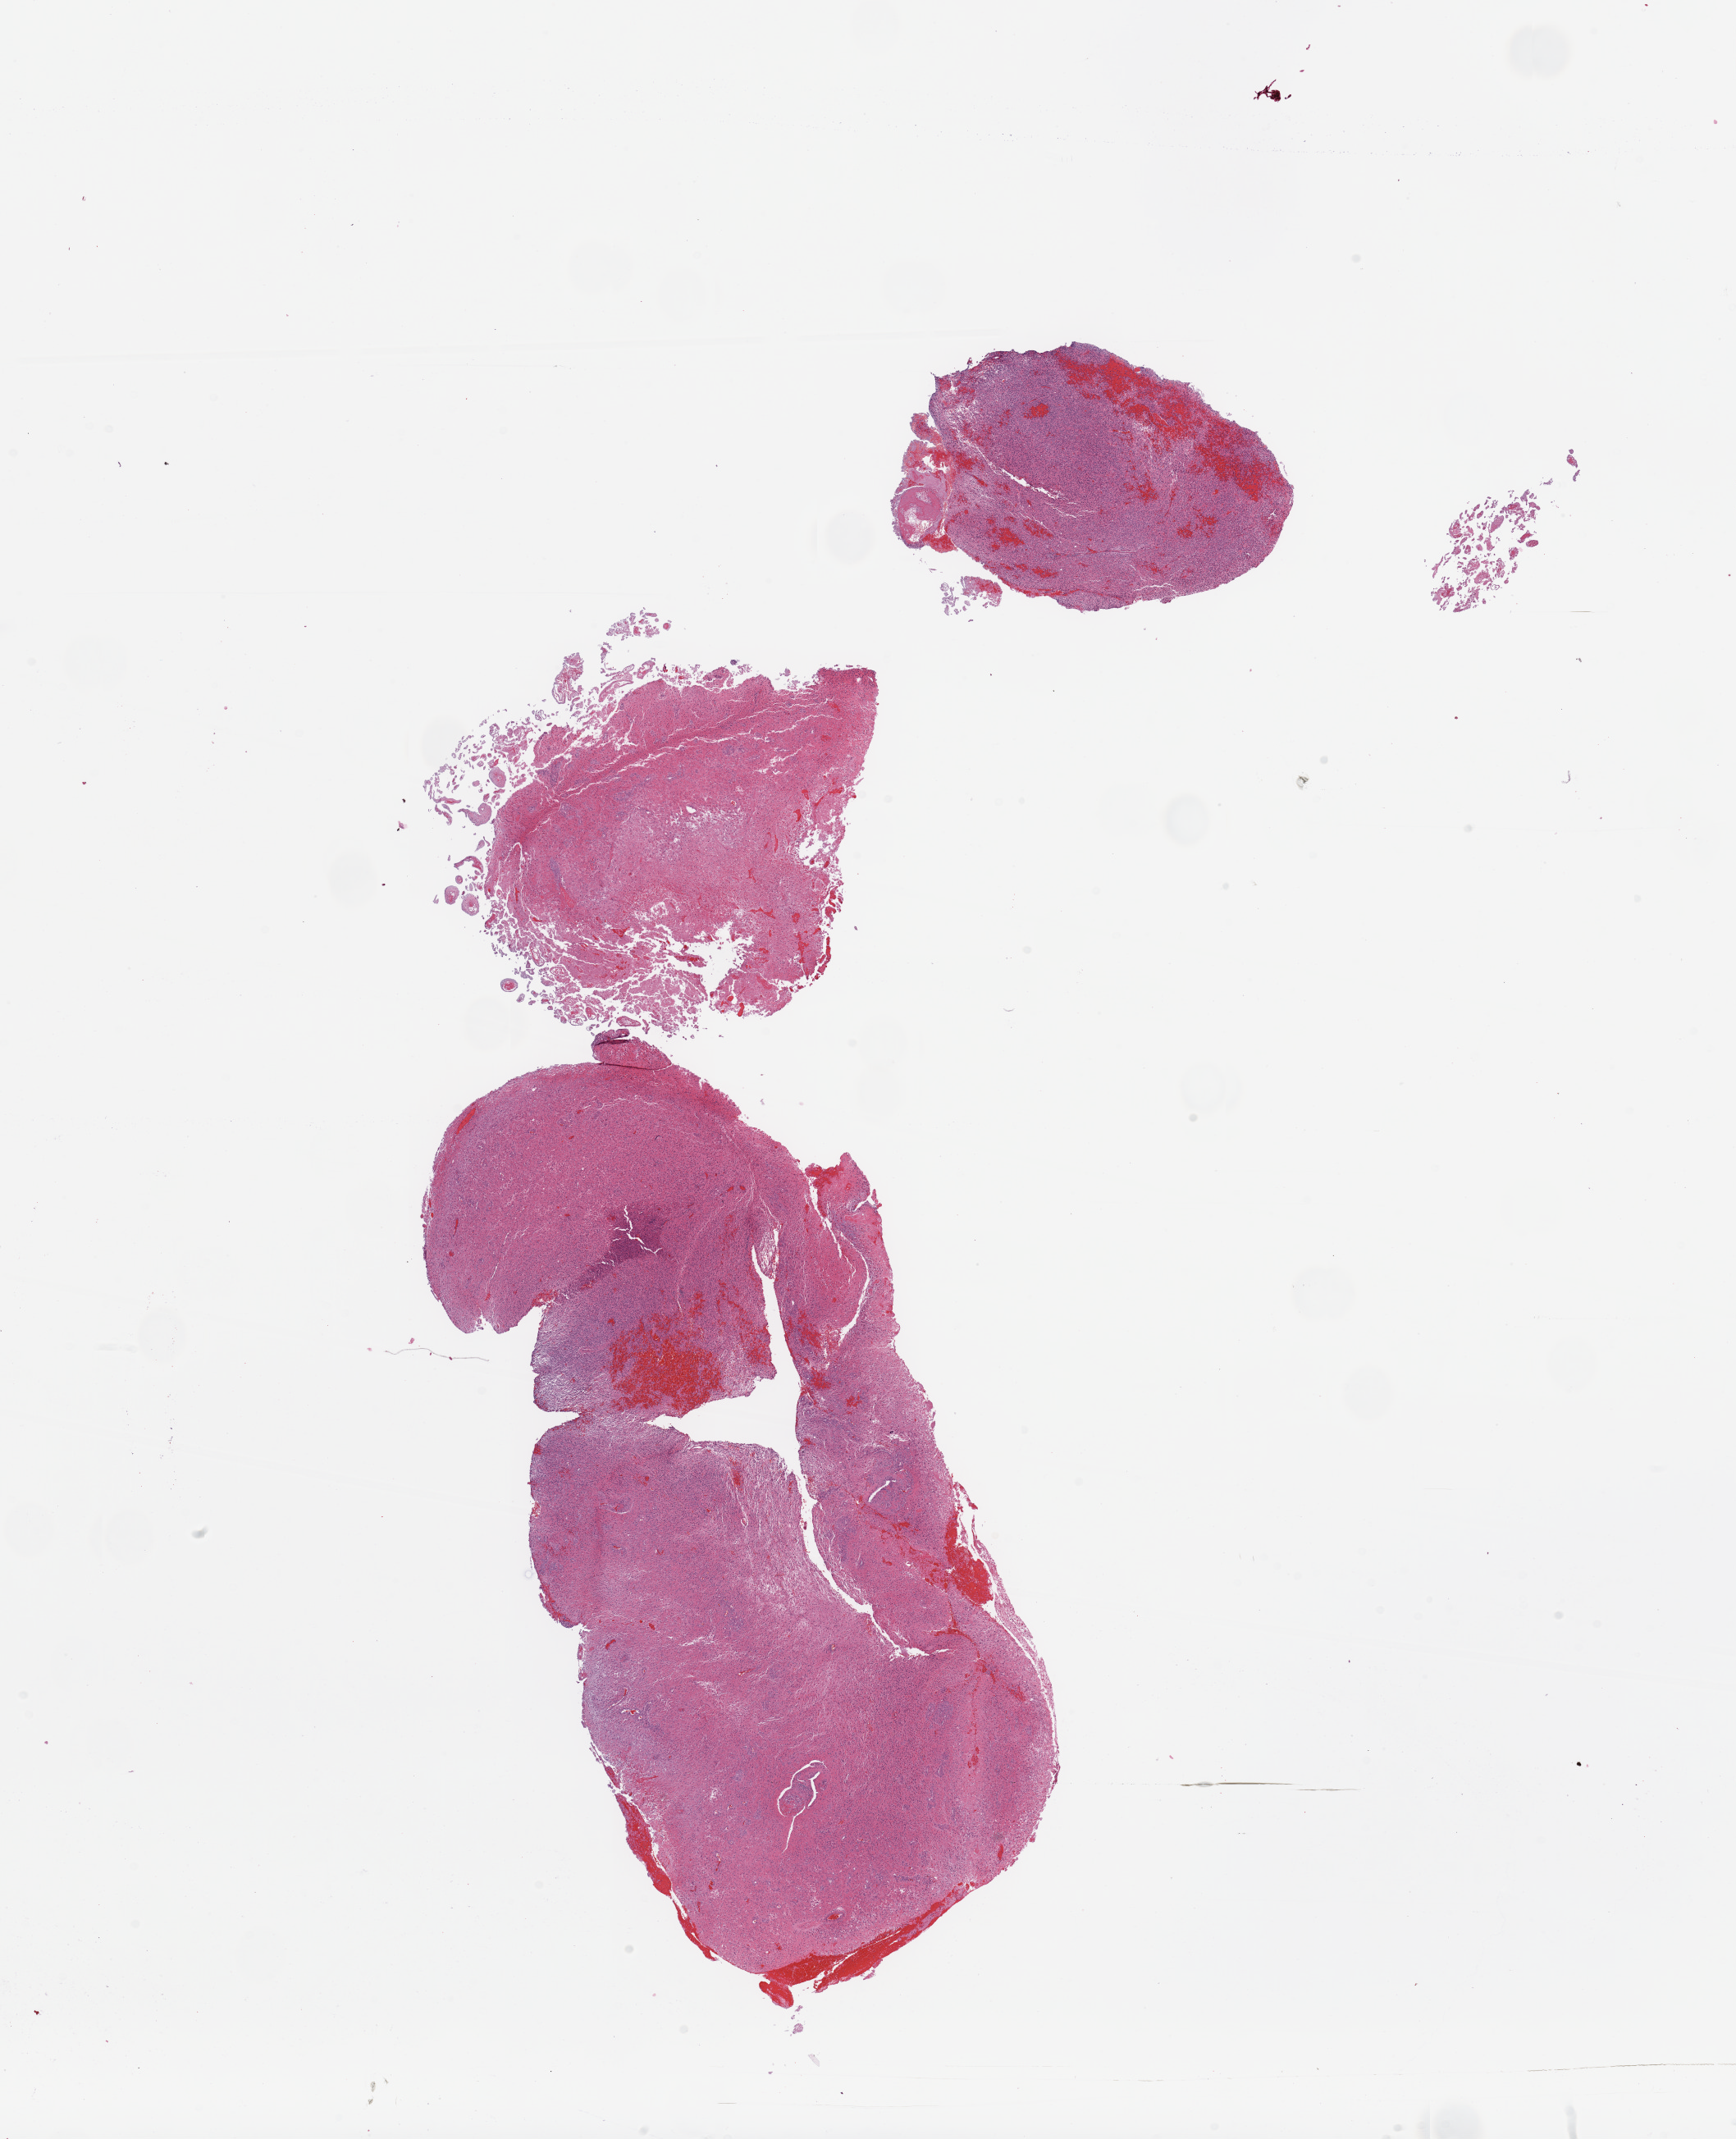
Digitized H&E-stained tissue section (whole slide), shown as a low-resolution overview of the whole scanned area (about 16.7 x 20.6 mm, slide scanned at 20x). Tumour tissue sample, brain. Patient: male, age 54 years.
Histologic diagnosis: Glioblastoma. Primary tumour site (as recorded): frontal lobe.